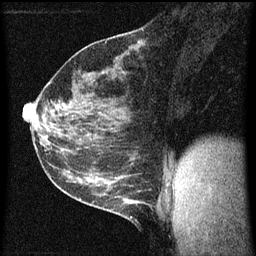
Breast MRI (dynamic contrast-enhanced), one sagittal slice; position 29 of 60 along the scan axis; dynamic contrast-enhanced series, image 2 of 3 at this slice position (ordered by acquisition); 1.5 T; TE 4.2 ms, TR 8 ms; 2 mm slice thickness; 256 × 256 image matrix, field of view 180 × 180 mm. Patient: female, 35 years.
Annotated regions visible in this slice (semi-automatically segmented with operator editing):
- analysis volume of interest (the breast-tissue region the enhancement analysis was run in; not a lesion): box from (x=106, y=182) to (x=149, y=223) px
- tumour enhancement mask (voxels above the 70 % enhancement threshold inside the analysis volume of interest): (x=130, y=216)–(x=133, y=219)